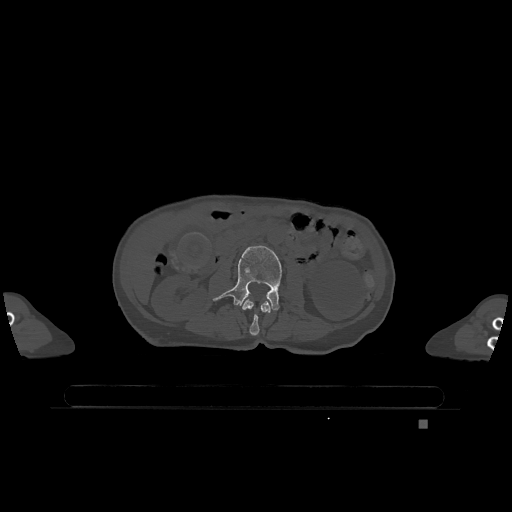
CT including the spine, one axial slice; position 375 of 1317 along the scan axis; bone window (W 1800 / L 400 HU); 0.5 mm slice thickness; 512 × 512 image matrix, field of view 500 × 500 mm. Patient: female, 74 years. Case-level facts recorded for this patient, not image findings: primary cancer: lung.
Outlined on this slice (semi-automatically segmented with operator editing):
- L2 vertebra: box from (x=241, y=299) to (x=272, y=336) px
- L3 vertebra: (x=213, y=245)–(x=282, y=310)